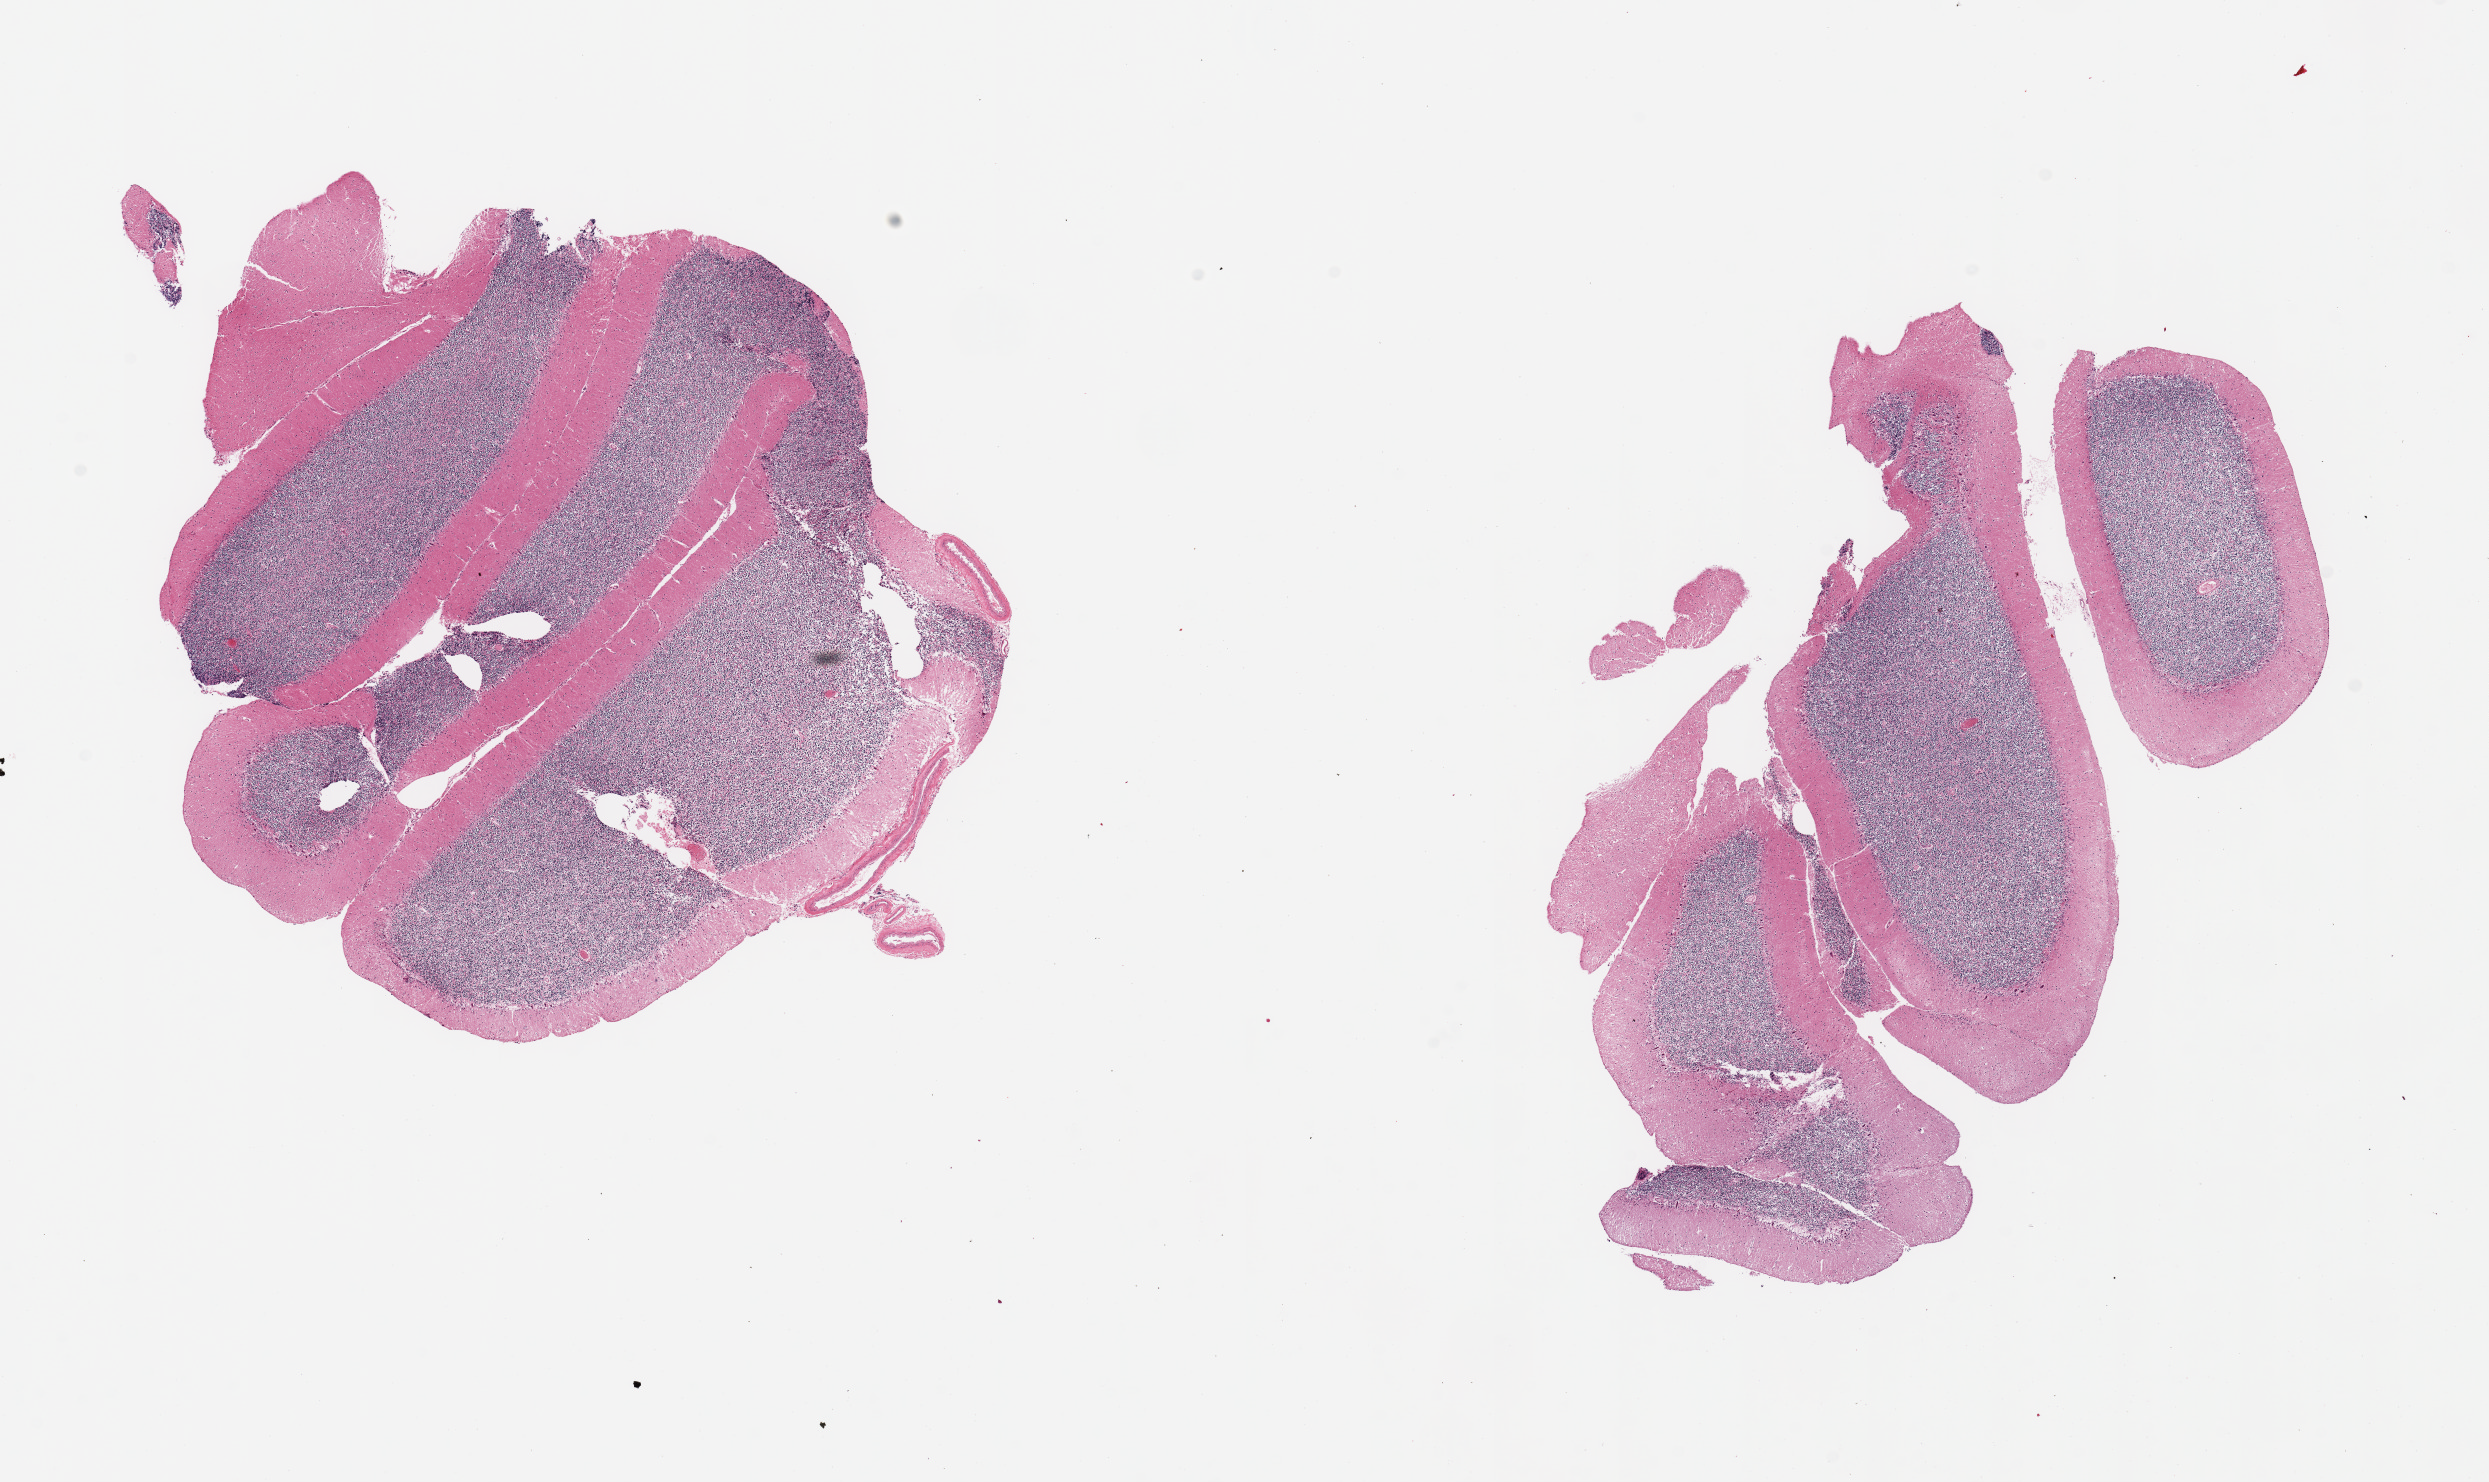
Haematoxylin and eosin whole-slide image, brightfield, a low-resolution overview of the entire scanned area, about 19.7 x 11.7 mm (slide scanned at 20x), PAXgene-fixed, paraffin-embedded tissue, sampled site (target tissue): cerebellum, donor tissue sample.
Reviewer comment on this tissue sample: 2 pieces, no abnormalities.